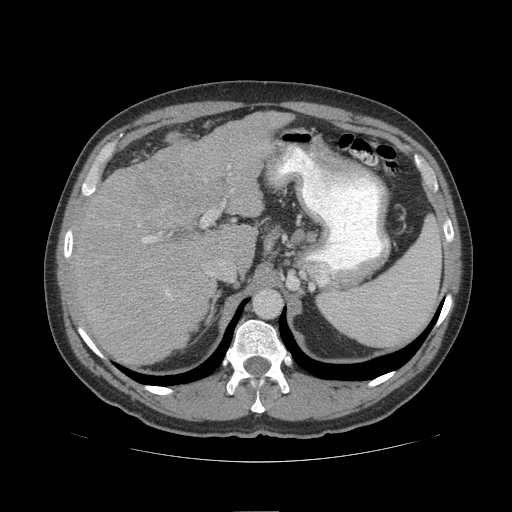
Contrast-enhanced abdominal CT (liver protocol), one axial slice. Slice 70 of 109 in the series (ordered by position). Reconstruction kernel STANDARD. Soft-tissue window (W 400 / L 40 HU). 512 × 512 image matrix. Case-level facts recorded for this patient, not image findings: diagnosis: hepatocellular carcinoma (patient treated with transarterial chemoembolisation; whether this scan precedes or follows treatment is not stated here); TNM stage (as recorded): Stage-IIIB; Child-Pugh class: A; tumour differentiation: poorly differentiated.
Outlined on this slice (semi-automatically segmented with operator editing):
- liver parenchyma outside the tumour (the mass and vessels are separate outlines, so this box may not span the whole liver): bounding box [x1, y1, x2, y2] px = [70, 110, 292, 364]
- liver vessels: [142, 190, 233, 296]